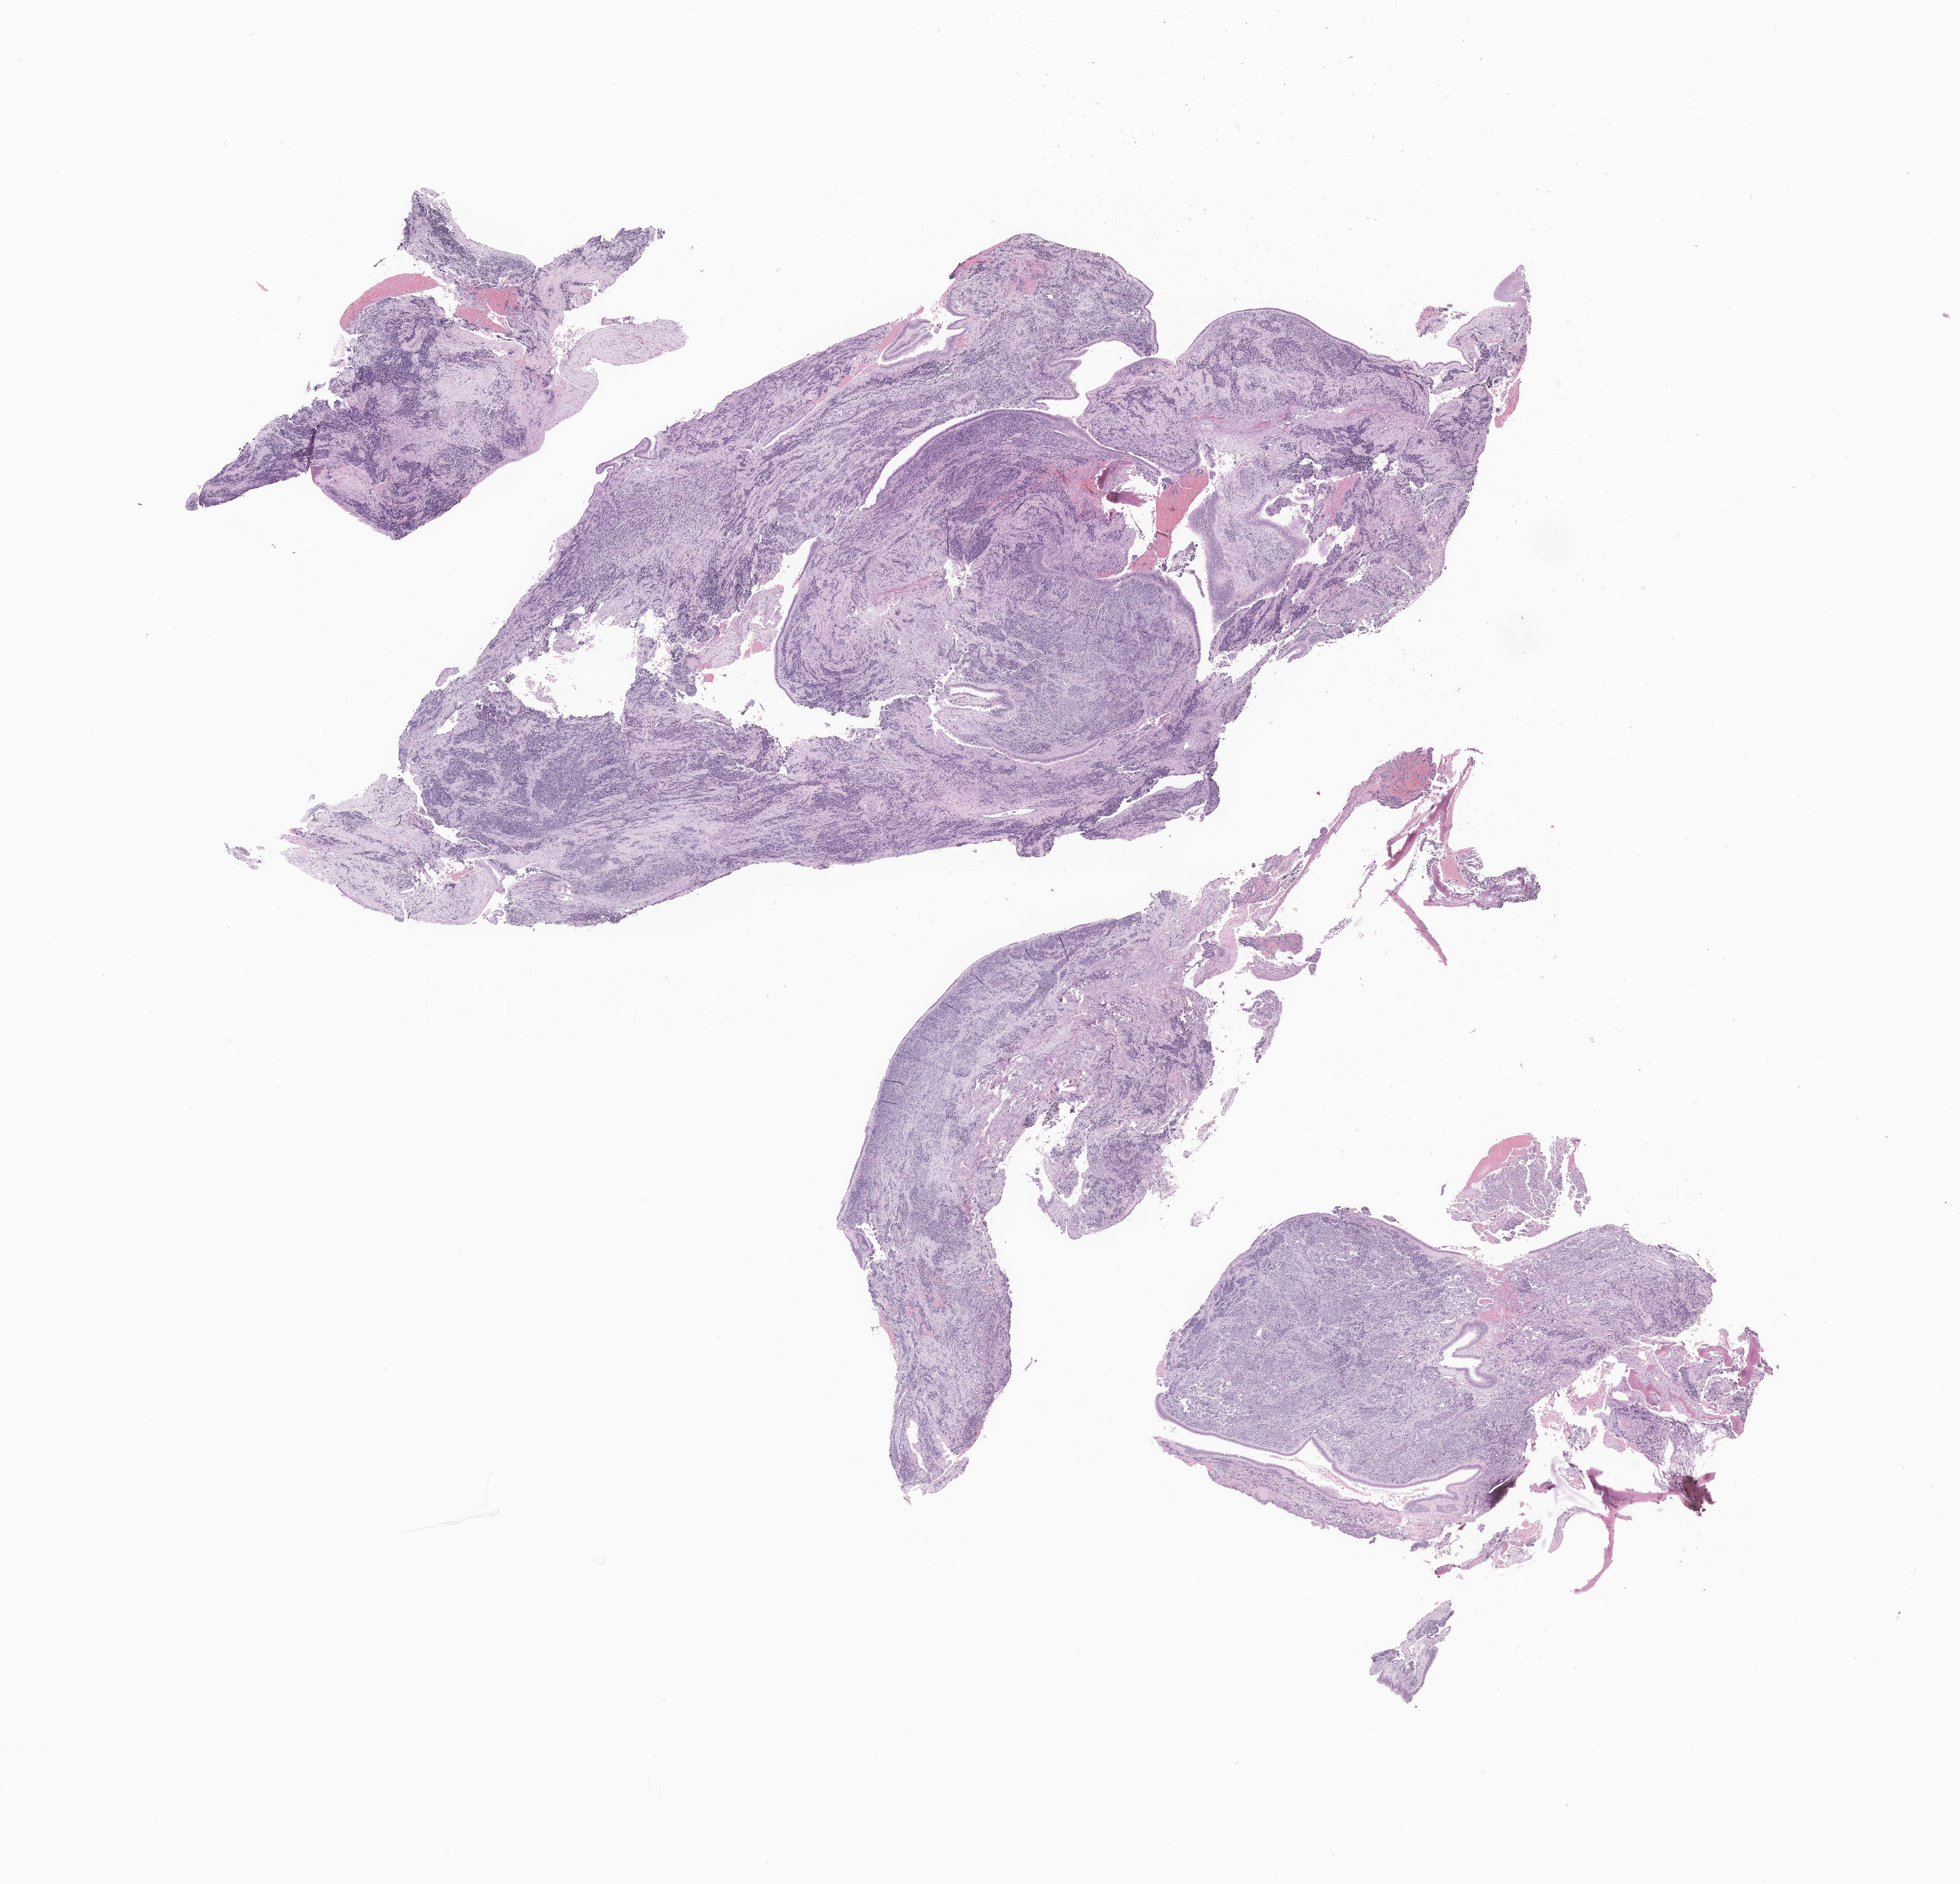
Digitized haematoxylin and eosin-stained section of tumor tissue from the ethmoid sinus, a low-resolution overview of the entire scanned area, about 19.8 x 19.0 mm, formalin-fixed, paraffin-embedded (FFPE) tissue. Male patient, age 225 months (18 years 9 months).
• diagnosis: Rhabdomyosarcoma, NOS